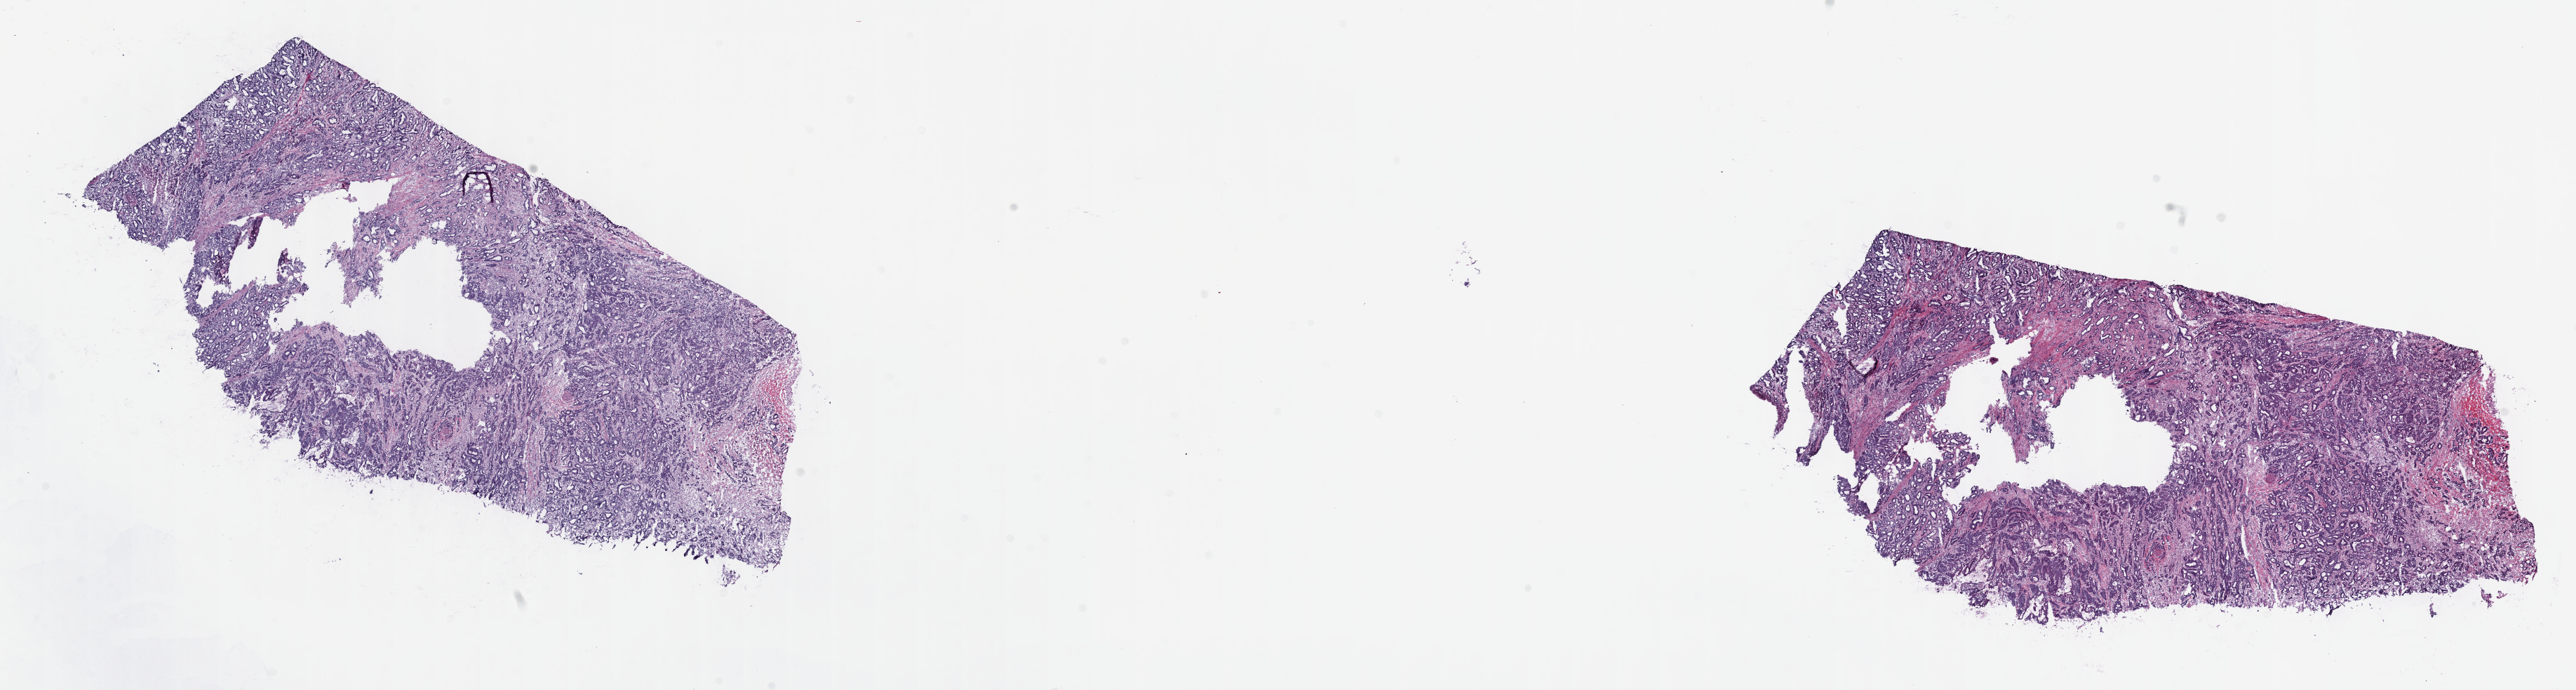
Digitized Hematoxylin and eosin (H&E) stained tissue section (whole slide) — a low-resolution overview of the entire scanned area, about 29.7 x 8.0 mm, frozen section from the top of the tissue portion, stomach, primary tumour sample. Male patient; age at initial diagnosis 70 years. Histologic grade: G2 (moderately differentiated). Slide review estimates, as recorded: tumour cells 100%, tumour nuclei 70%, normal cells 0%, stromal cells 0%, necrosis 0%. Inflammatory infiltration, as recorded: lymphocyte infiltration 4%, monocyte infiltration 0%, neutrophil infiltration 0%.
- histologic diagnosis: Adenocarcinoma, intestinal type (body of stomach)
- lymph nodes positive (case pathology): 5 of 33 examined
- AJCC pathologic stage: IIIC